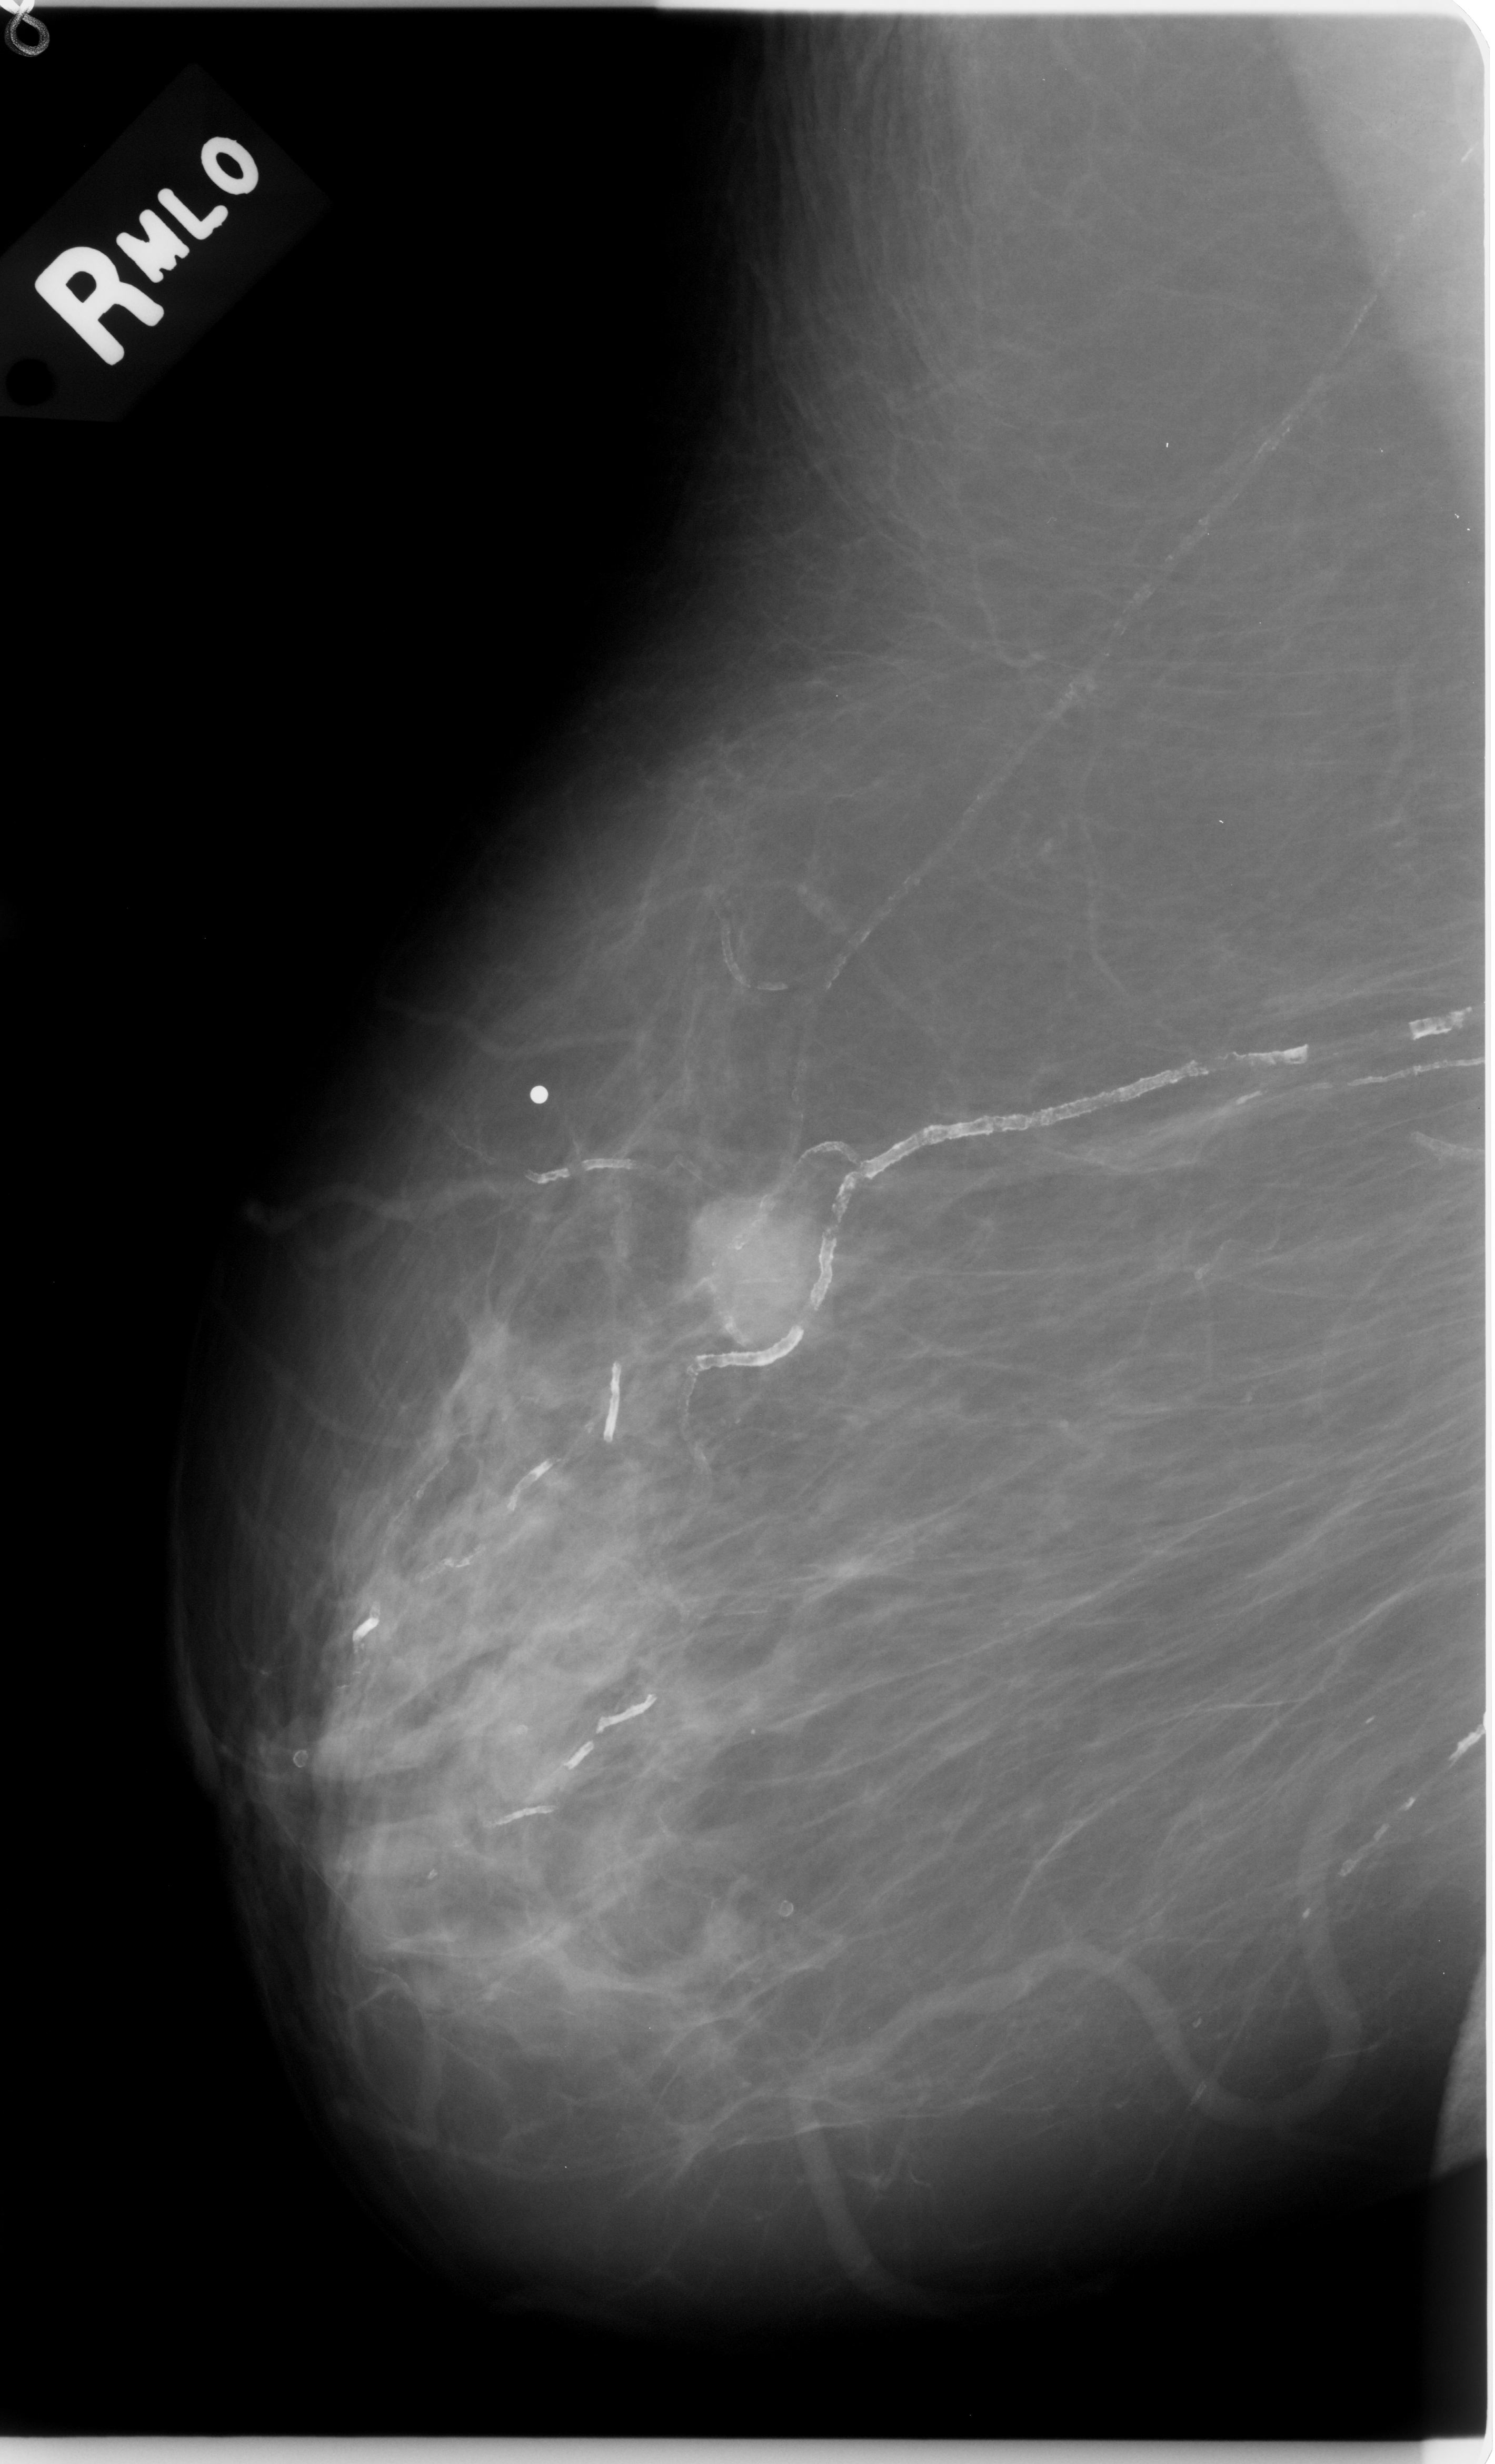
Digitized screen-film mammogram. Right breast. Mediolateral oblique (MLO) view. Breast composition: almost entirely fatty (BI-RADS density category 1 of 4). 1495 × 2464 image matrix.
Expert-marked regions of interest on this image (one box per marked abnormality):
- mass, shape irregular, margins microlobulated; BI-RADS assessment category 5; subtlety rating 5 on a 1 (subtle) to 5 (obvious) scale; pathology (as recorded): malignant: bounding box [x1, y1, x2, y2] px = [686, 1164, 873, 1376]